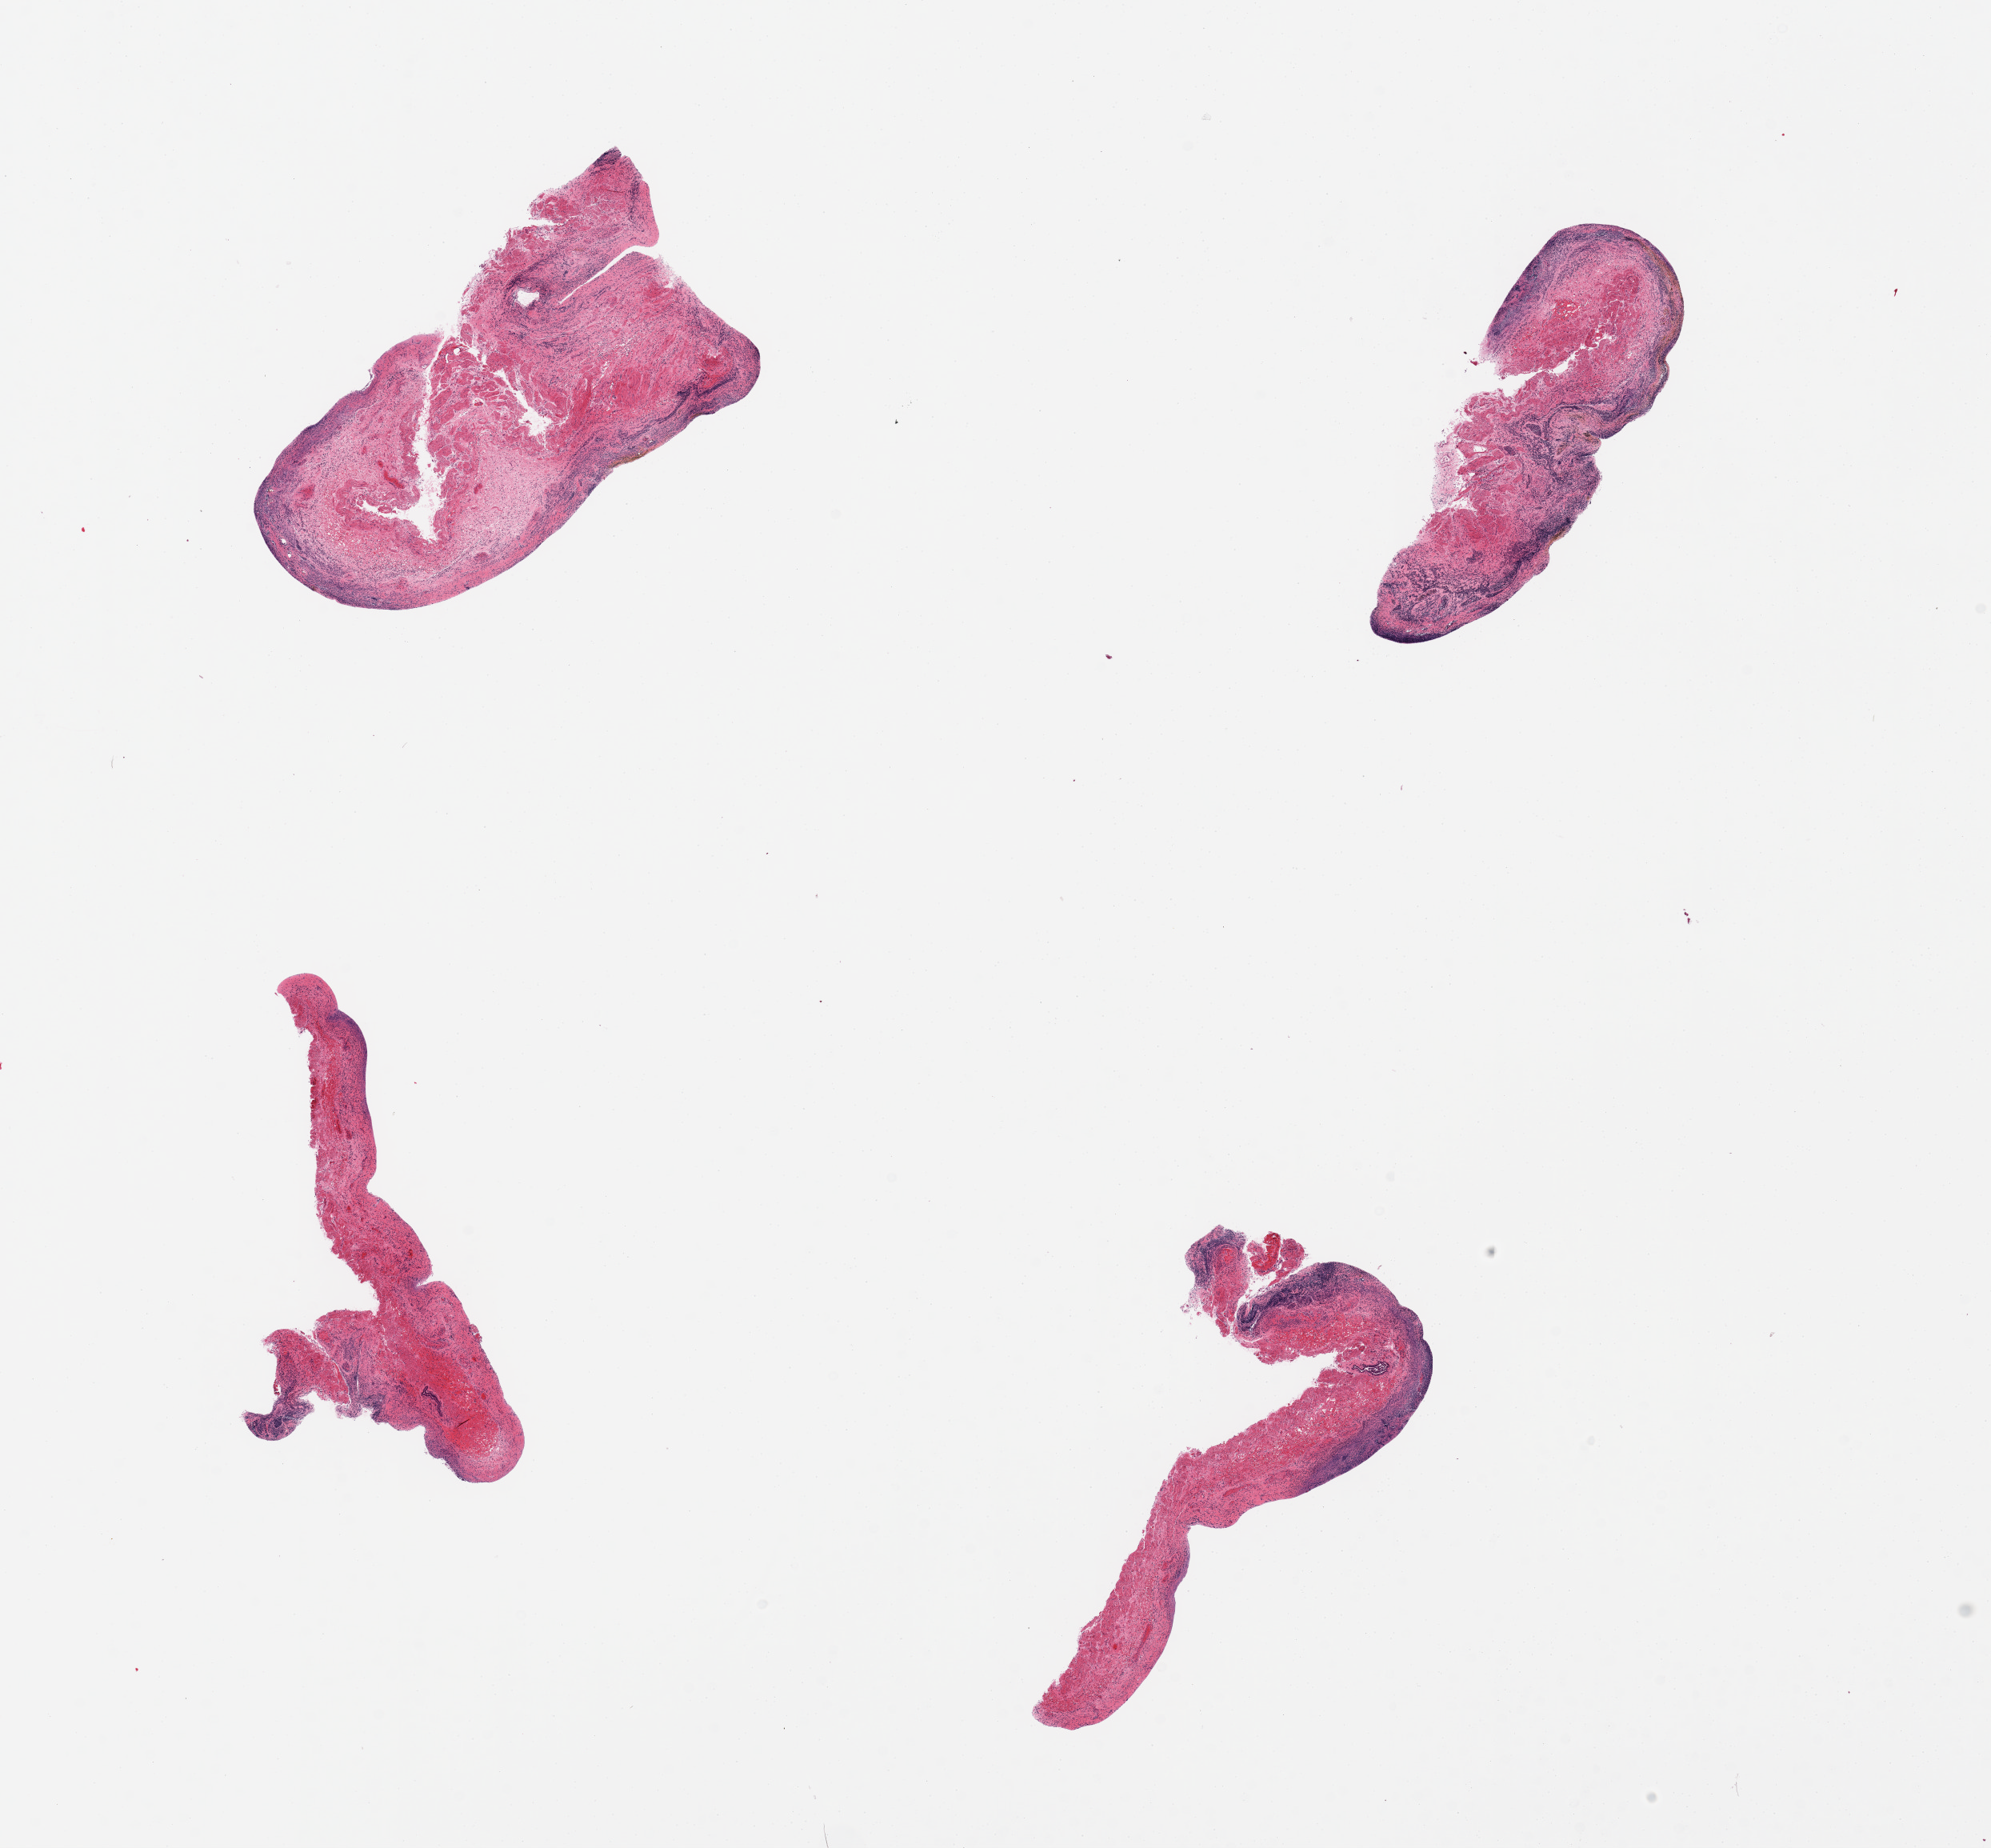
Whole-slide image, haematoxylin and eosin stain, shown as a low-resolution overview of the whole scanned area (about 19.7 x 18.3 mm, slide scanned at 20x); PAXgene-fixed paraffin-embedded (PFPE) section; sampled site (target tissue): esophageal mucous membrane; tissue donor sample.
Review note (as recorded): 4 pieces, markedly autolyzed; mucosa largely sloughed.